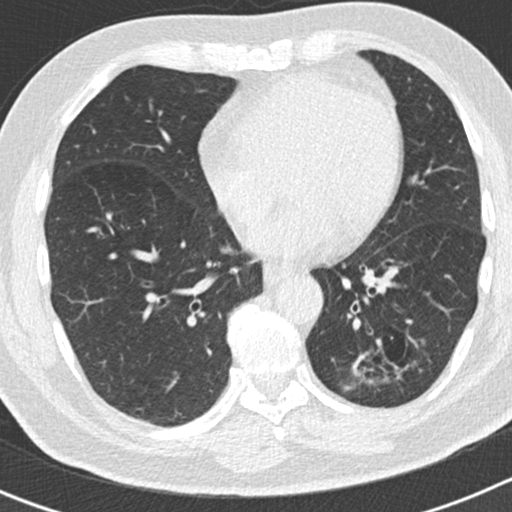
Axial slice from a low-dose chest CT screening exam, second annual screen, lung window (W 1500 / L -600 HU), 2 mm slice thickness, 120 kVp, 512 × 512 image matrix, field of view 300 × 300 mm. Male participant, aged 66 years at enrolment. Former smoker at enrolment.
• Expert-annotated lung lesion, bounding box <345,323,417,402> (left, top, right, bottom; pixels).
• Screening reader's record for this exam (one nodule recorded; not confirmed to be the boxed lesion): non-calcified nodule or mass ≥4 mm, left lower lobe, 50 × 33 mm, smooth margins, pre-existing on the prior screen: yes; interval growth: yes.
• Official screen result: positive, other.
• Participant outcome: lung cancer diagnosed 440 days after this screen — adenocarcinoma, NOS, left lower lobe, poorly differentiated (G3), stage IB (AJCC 6th edition), 38 mm at pathology.